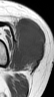
MRI of an extremity soft-tissue mass, one axial slice. Position 25 of 42 along the scan axis. MR volume resampled by the dataset authors to the PET/CT grid (not the native acquisition matrix). 3.27 mm slice thickness. 54 × 97 image matrix. Female patient. From the clinical record (not read from this slice): histological type: spindle cell suggestive of biphasic synovial sarcoma; grade: intermediate; site of the primary tumour: left knee.
Outlined on this slice (expert contour drawn on MRI and transferred to this co-registered scan by the dataset authors):
- gross tumour volume including surrounding oedema: box from (x=14, y=16) to (x=45, y=67) px
- gross tumour volume (mass): (x=17, y=18)–(x=45, y=67)